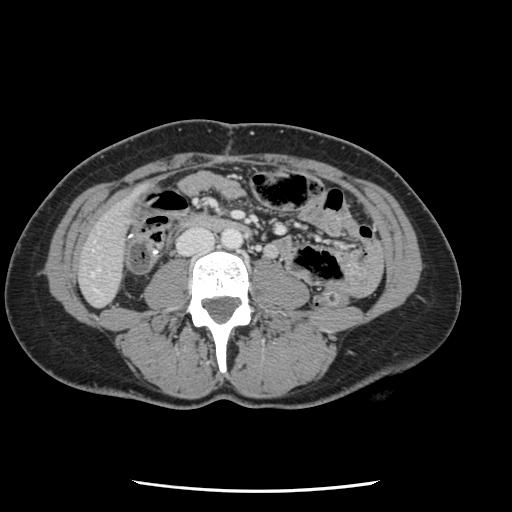
Contrast-enhanced abdominal CT, one axial slice; position 12 of 134 along the scan axis; 120 kVp; soft-tissue window (W 400 / L 40 HU); 512 × 512 image matrix, field of view 330 × 330 mm. Female patient, age 43 years. Case-level facts recorded for this patient, not image findings: diagnosis: colorectal cancer liver metastases, imaged before liver resection; multiple liver metastases: yes; largest metastasis: 3.4 cm.
Structures marked on this image (outlined manually by an expert reader):
- liver: bounding box <80,199,132,306> (left, top, right, bottom; pixels)
- planned liver remnant (the part of the liver to remain after resection): <80,198,132,306>